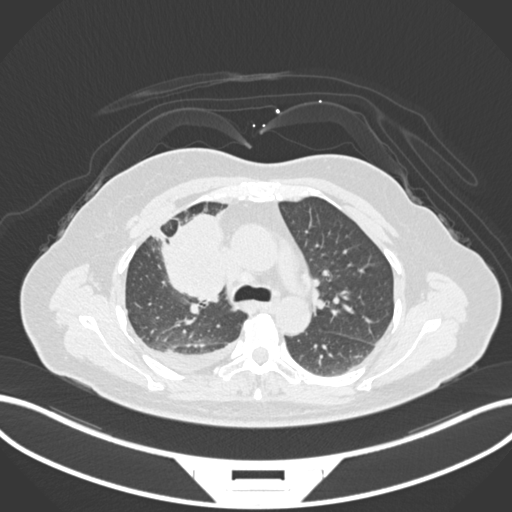
Chest CT, one axial slice. Position 101 of 172 along the scan axis. Lung window (W 1500 / L -600 HU). 512 × 512 image matrix. Female patient, age 52 years. Case-level facts recorded for this patient, not image findings: clinical TNM (as recorded): T3 N1 M1.
Structures marked on this image (rectangle marked by the reading radiologist):
- lung tumour (recorded histology: adenocarcinoma): bounding box [x1, y1, x2, y2] px = [151, 204, 229, 303]